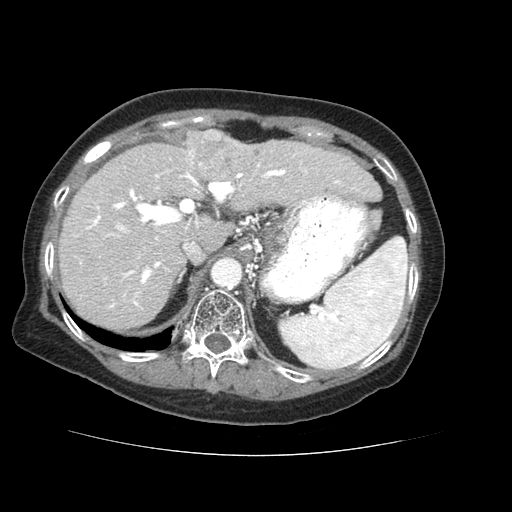
Contrast-enhanced abdominal CT (liver protocol), one axial slice. Position 43 of 73 along the scan axis. Reconstruction kernel STANDARD. Soft-tissue window (W 400 / L 40 HU). 2.5 mm slice thickness. 512 × 512 image matrix. From the clinical record (not read from this slice): diagnosis: hepatocellular carcinoma (patient treated with transarterial chemoembolisation; whether this scan precedes or follows treatment is not stated here); TNM stage (as recorded): Stage-IVB; Child-Pugh class: A; tumour differentiation: well differentiated; tumour nodularity: uninodular.
Annotated regions visible in this slice (semi-automatic segmentation, software-assisted and operator-edited):
- liver parenchyma outside the tumour (the mass and vessels are separate outlines, so this box may not span the whole liver): bounding box (x1, y1, x2, y2) in pixels: (58, 129, 380, 330)
- mass: (183, 130, 246, 181)
- liver vessels: (75, 150, 355, 308)